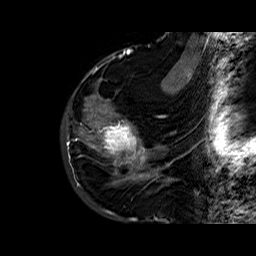
Breast MRI (dynamic contrast-enhanced), one sagittal slice. Slice 17 of 60 in the series (ordered by position). Dynamic contrast-enhanced series, time point 2 of 6 at this slice position (early post-contrast). 1.5 T. TE 6.4 ms, TR 32.8 ms. 4 mm slice thickness. 256 × 256 image matrix, field of view 200 × 200 mm. Female patient. Case-level facts recorded for this patient, not image findings: setting: breast cancer imaged before/during neoadjuvant chemotherapy; receptor status: HR-positive, HER2-negative.
Outlined on this slice (semi-automatic segmentation, software-assisted and operator-edited):
- analysis volume of interest (the breast-tissue region the enhancement analysis was run in; not a lesion): bounding box [x1, y1, x2, y2] px = [86, 77, 163, 177]
- tumour enhancement mask (voxels above the 100 % enhancement threshold inside the analysis volume of interest): [86, 99, 145, 164]